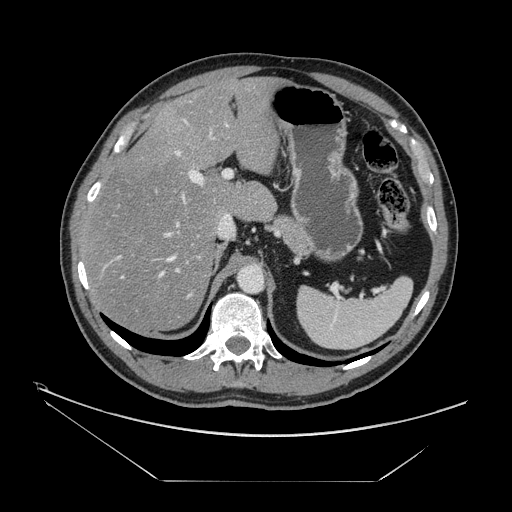
Contrast-enhanced abdominal CT, one axial slice; reconstruction kernel STANDARD; 120 kVp; intravenous contrast given; soft-tissue window (W 400 / L 40 HU); 2.5 mm slice thickness; 512 × 512 image matrix. Male patient, age 65 years. Case-level facts recorded for this patient, not image findings: diagnosis: colorectal cancer liver metastases, imaged before liver resection; multiple liver metastases: yes; largest metastasis: 4.2 cm; chemotherapy before resection: yes.
Outlined on this slice (manually delineated by an expert):
- hepatic veins: bounding box (x1, y1, x2, y2) in pixels: (121, 121, 186, 279)
- liver: (84, 79, 278, 330)
- planned liver remnant (the part of the liver to remain after resection): (84, 79, 278, 330)
- portal vein (with intrahepatic branches): (112, 151, 232, 280)